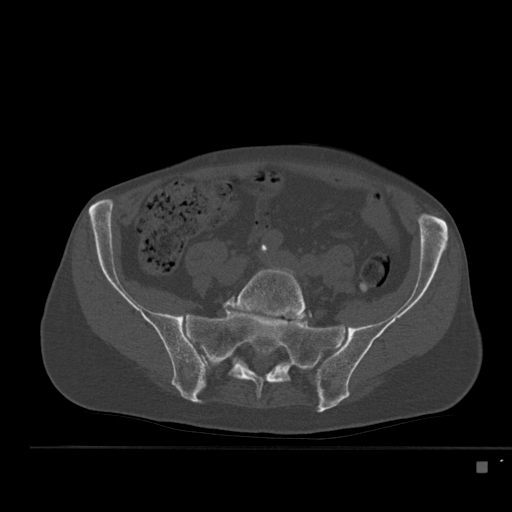
CT including the spine, one axial slice. Slice 112 of 517 in the series (ordered by position). Reconstruction kernel Br40s. 120 kVp. Bone window (W 1800 / L 400 HU). 1.5 mm slice thickness. 512 × 512 image matrix, field of view 408 × 408 mm. Male patient, age 70 years. Case-level facts recorded for this patient, not image findings: primary cancer: renal; vertebrae with lytic lesions (as recorded): T4, T6, T10, T12, L3, L4, L5.
Outlined on this slice (semi-automatically segmented with operator editing):
- L5 vertebra: bounding box [x1, y1, x2, y2] px = [225, 267, 312, 322]